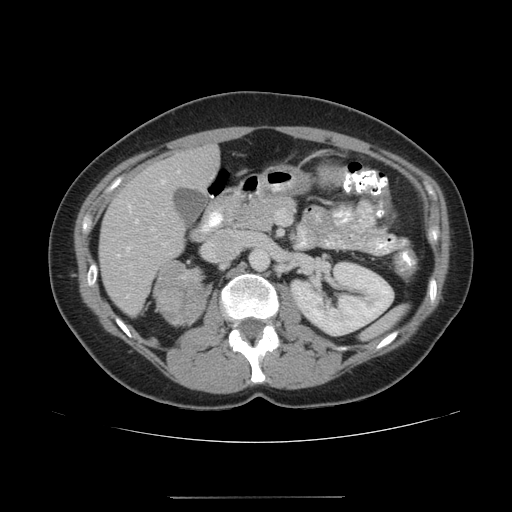
Contrast-enhanced abdominal CT, one axial slice. Slice 99 of 161 in the series (ordered by position). Intravenous contrast given. Soft-tissue window (W 400 / L 40 HU). 3.75 mm slice thickness. 512 × 512 image matrix, field of view 380 × 380 mm. Female patient. Case-level facts recorded for this patient, not image findings: diagnosis: adrenocortical carcinoma; tumour side: right adrenal; tumour size at pathology: 9 cm; Ki-67 index: 14 %; stage (as recorded): 3.
Outlined on this slice (semi-automatic segmentation, software-assisted and operator-edited):
- mass: bounding box (x1, y1, x2, y2) in pixels: (155, 261, 211, 325)